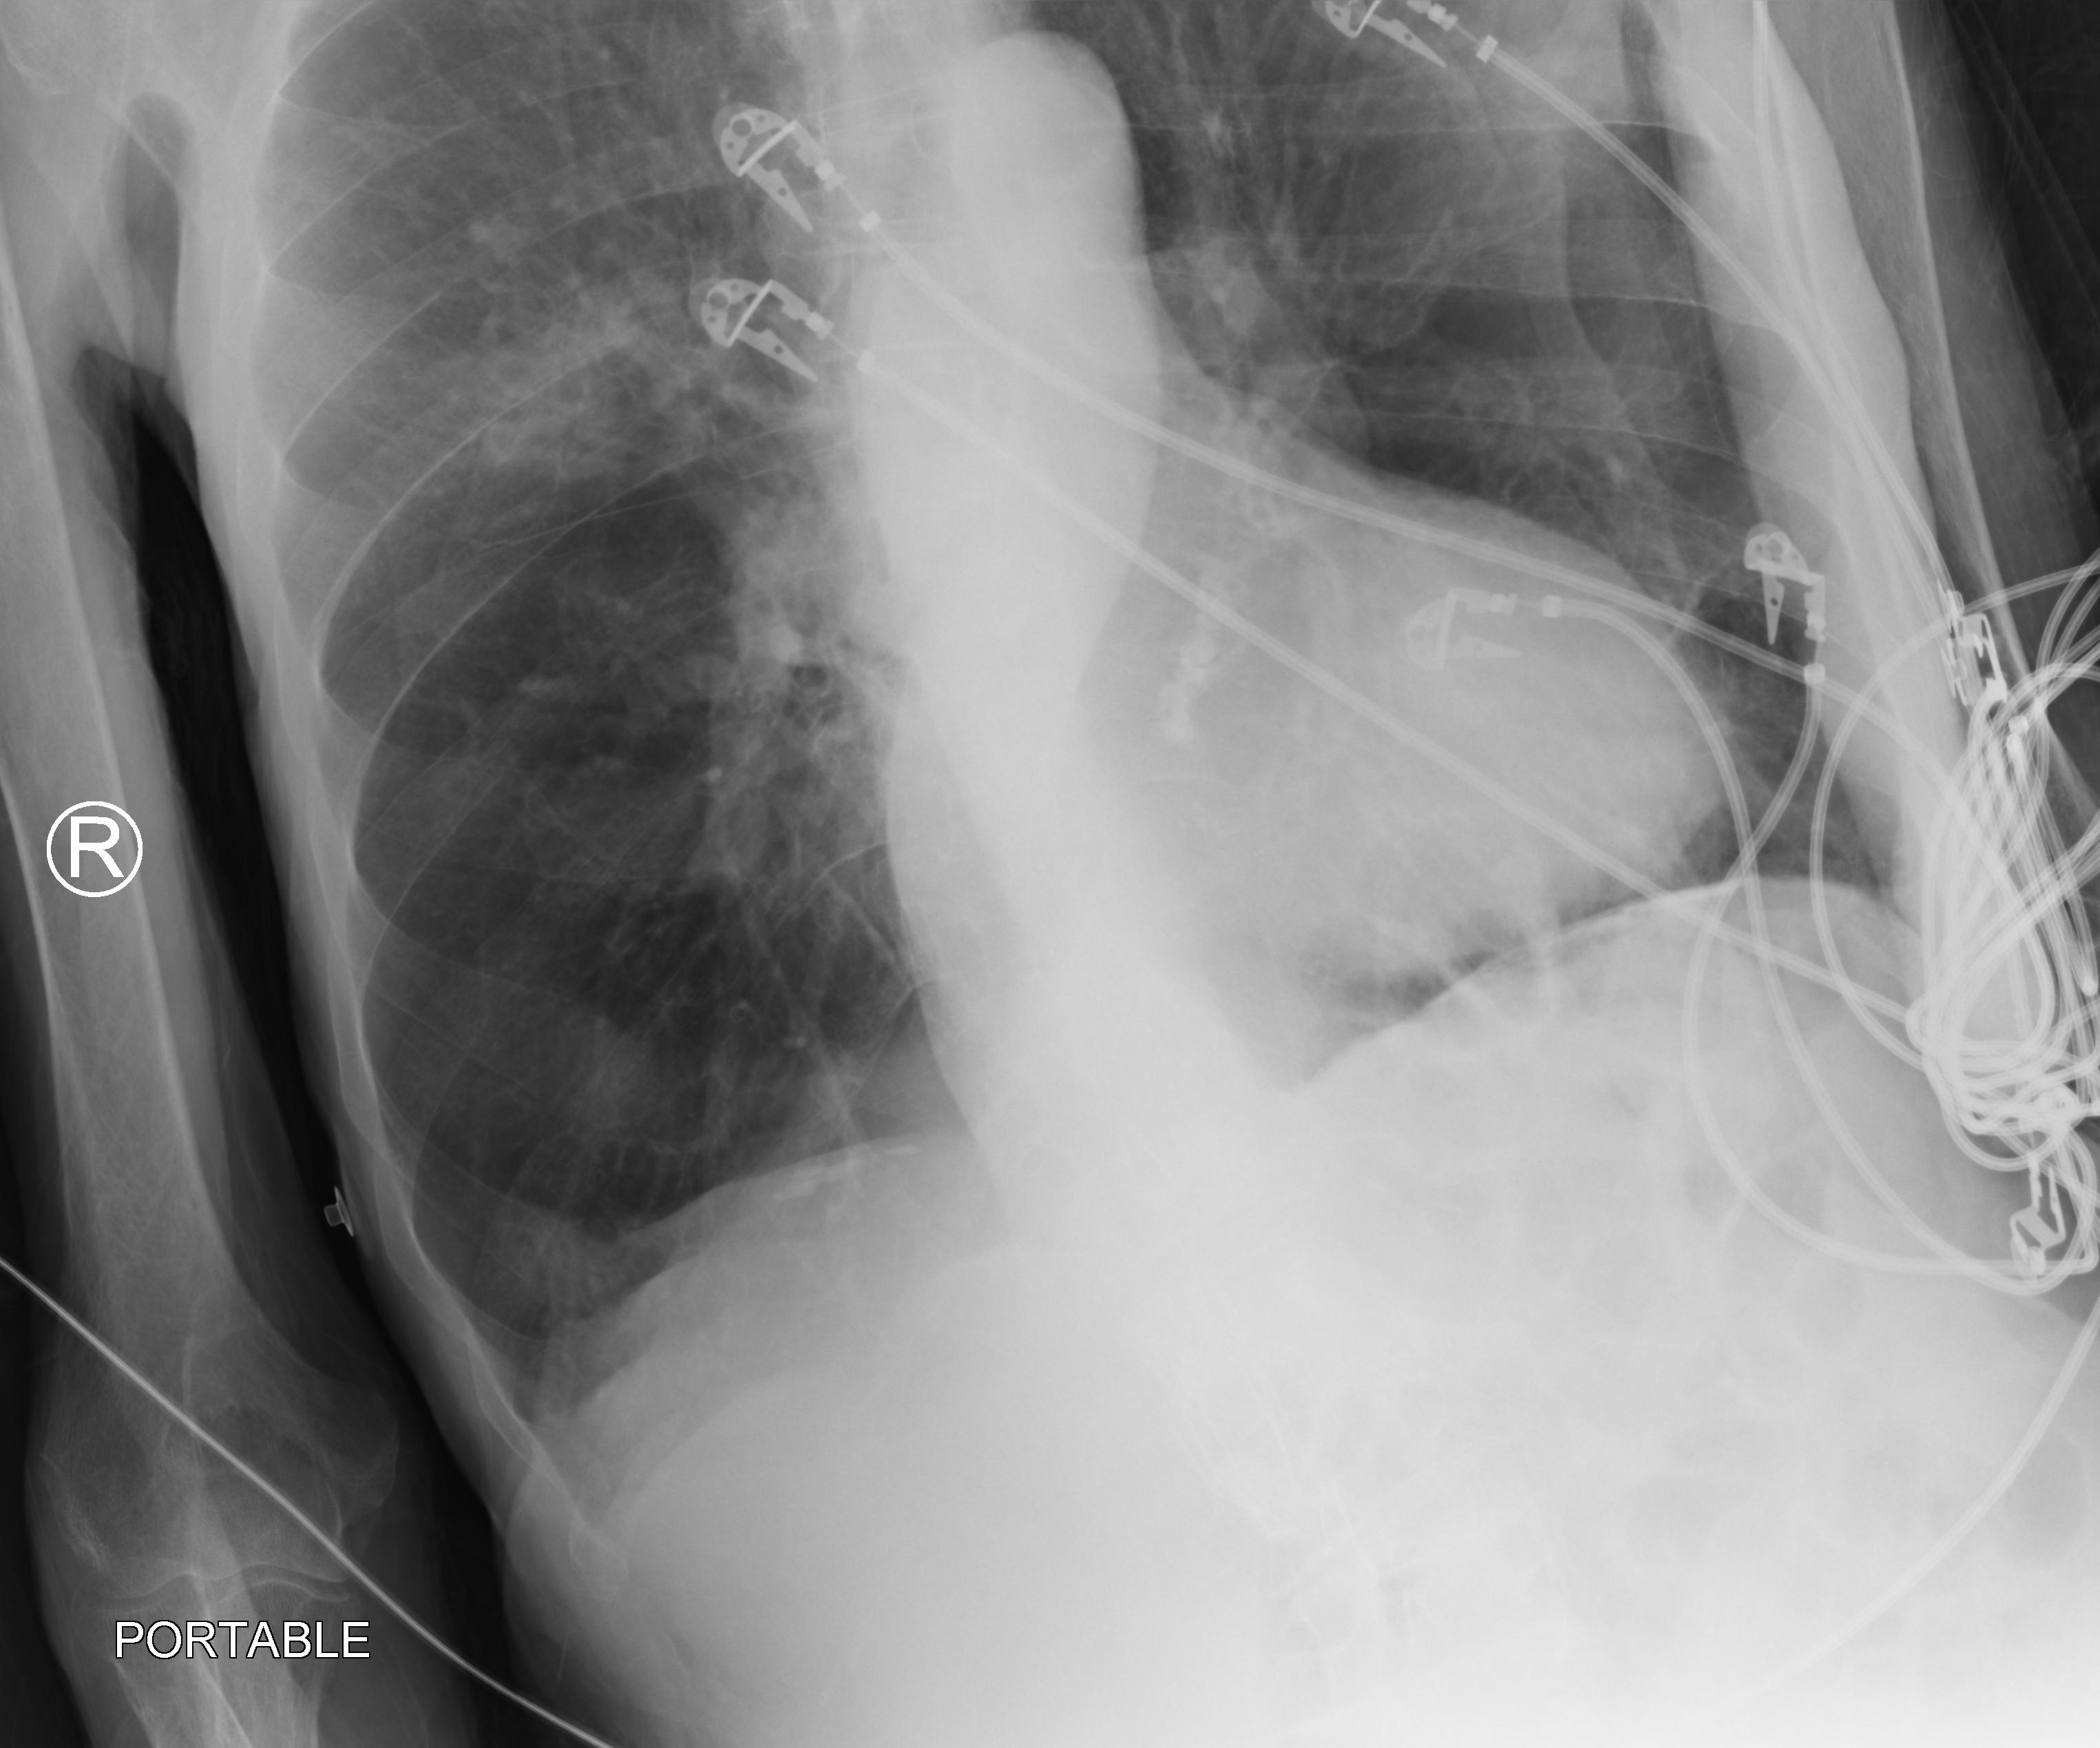
Bedside chest radiograph (computed radiography). Patient hospitalised with COVID-19; male, aged 75–90 years.
From the hospital-stay record, not from the radiograph (when in the stay this image was taken is not recorded): other chronic lung disease (admission record): no; admitted to intensive care during this hospital stay: no; length of hospital stay: 6 days.